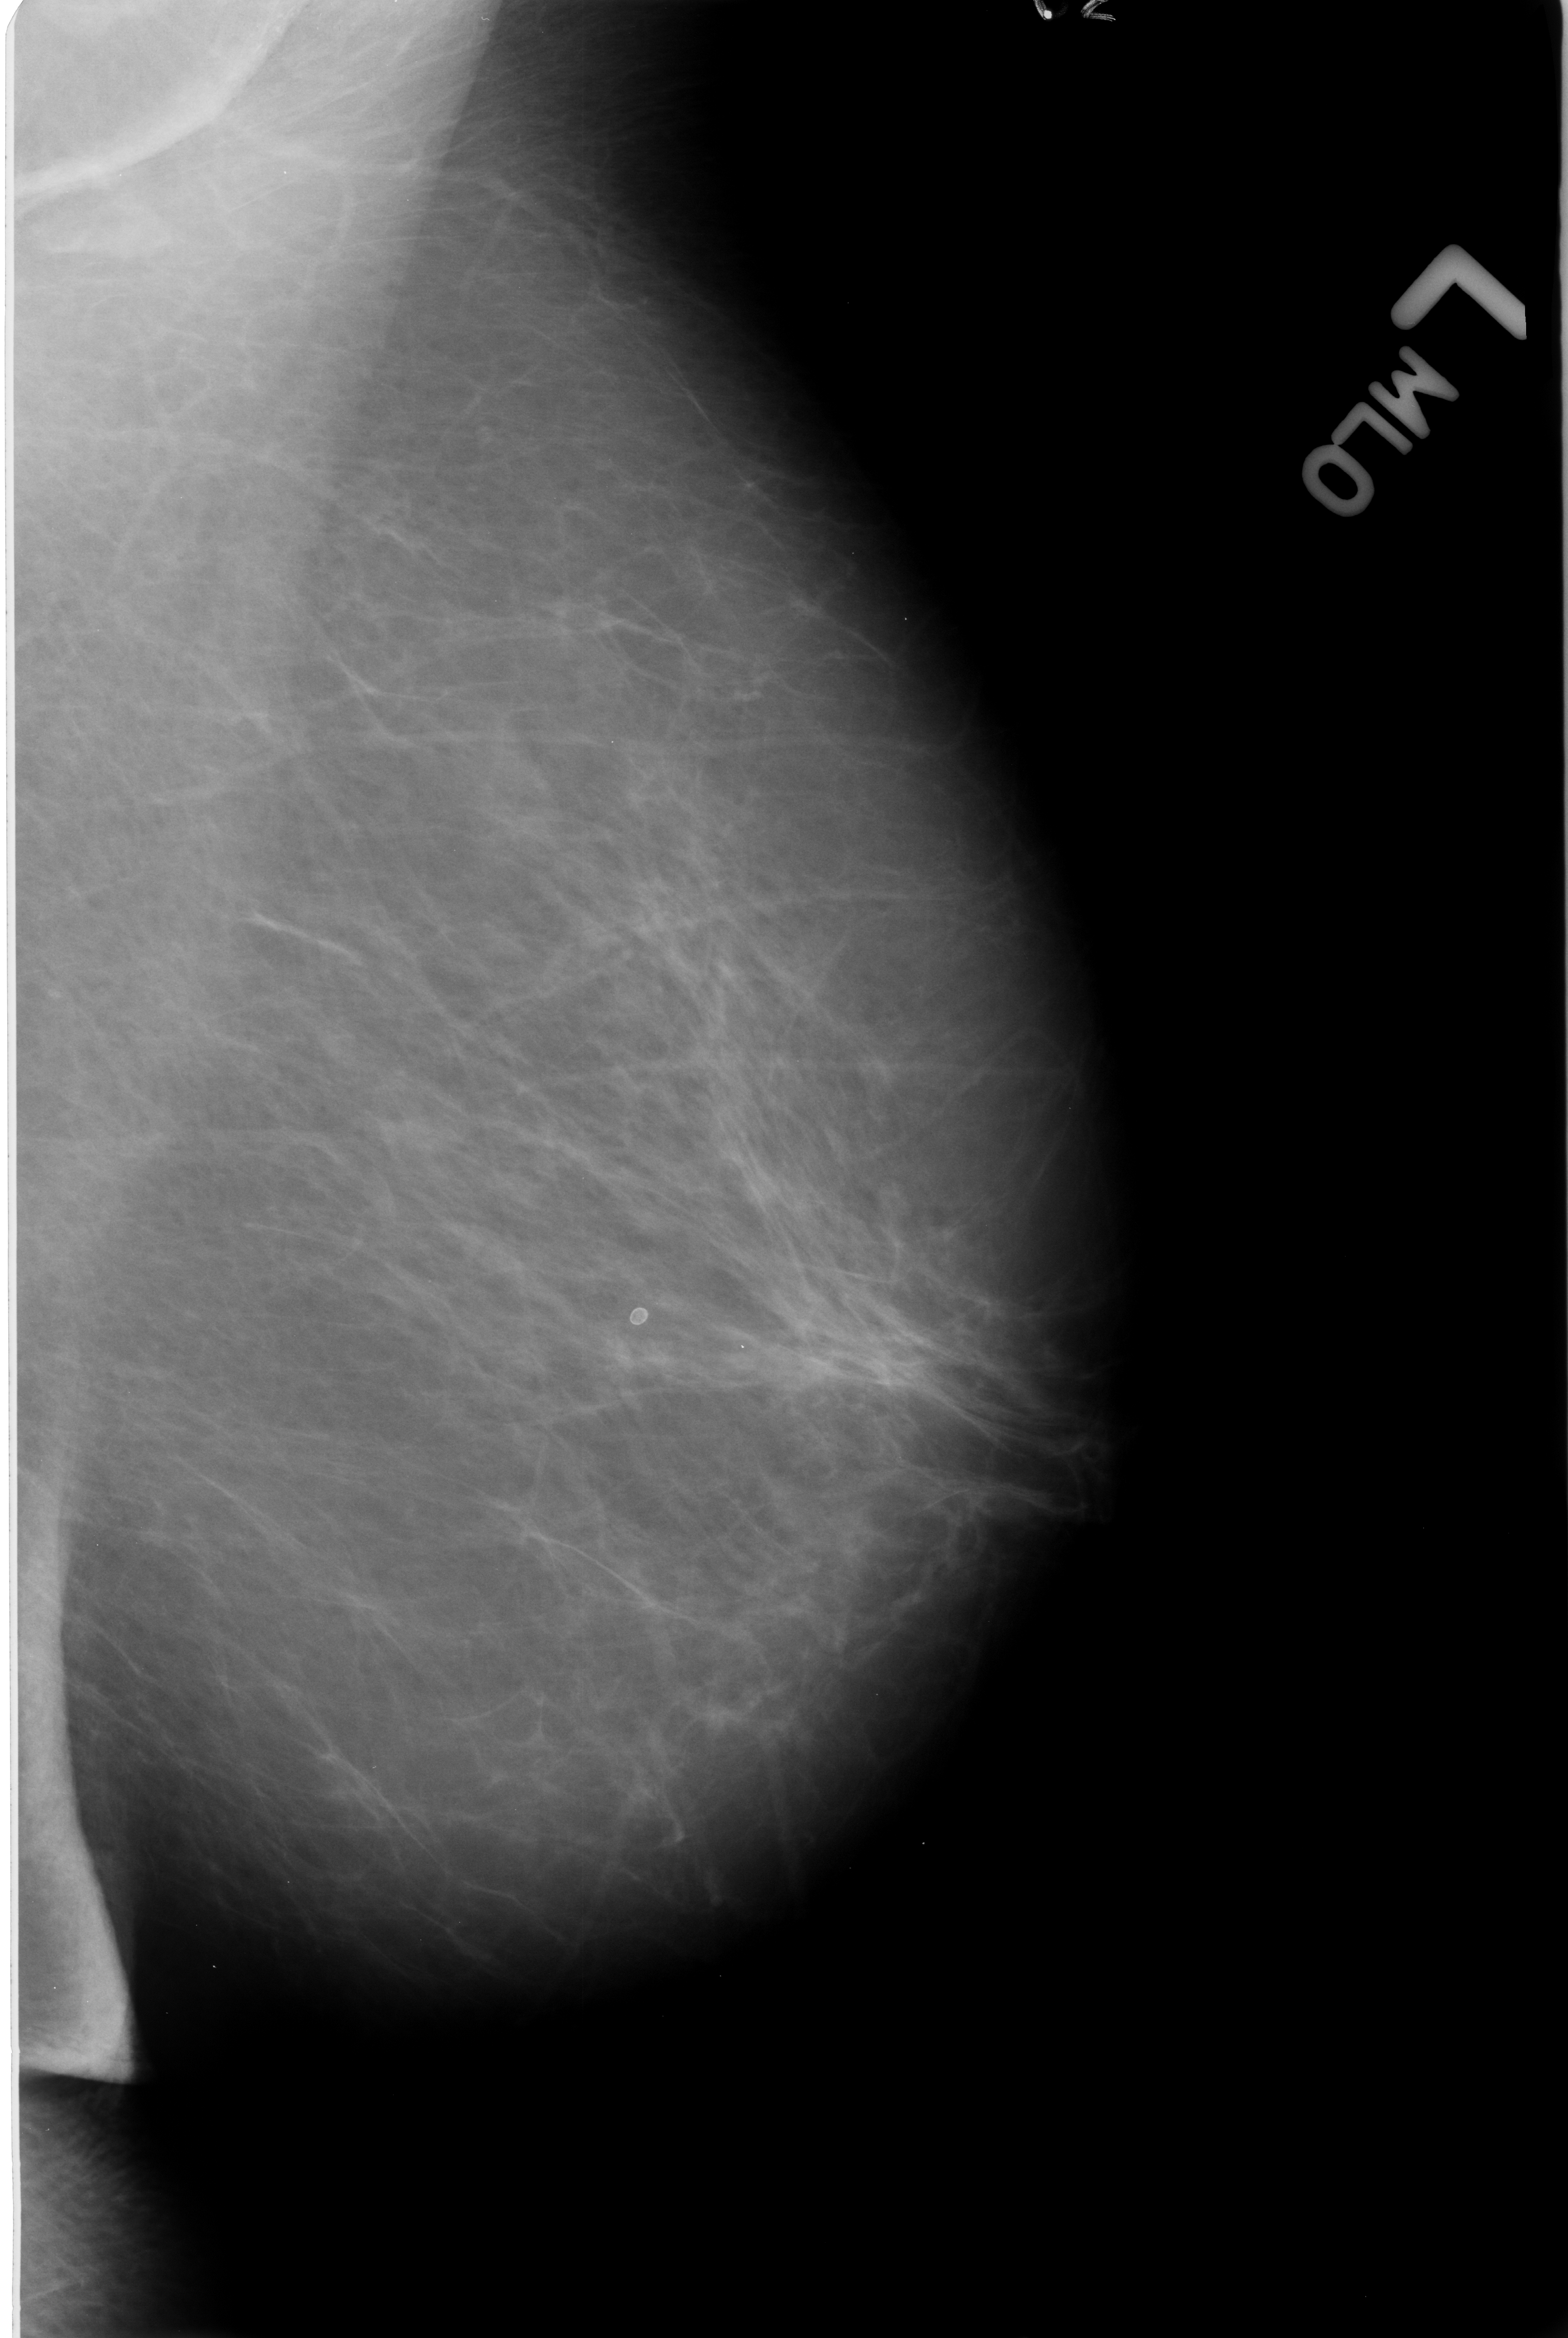
Digitized screen-film mammogram. Left breast. MLO view. BI-RADS breast density category 2 (scale 1–4). 1568 × 2338 image matrix.
Expert-marked regions of interest on this film, with their recorded descriptors:
- calcifications, morphology lucent center; BI-RADS assessment category 2; outcome (as recorded, no biopsy): benign without callback (not worked up further): box from (x=608, y=1299) to (x=655, y=1333) px